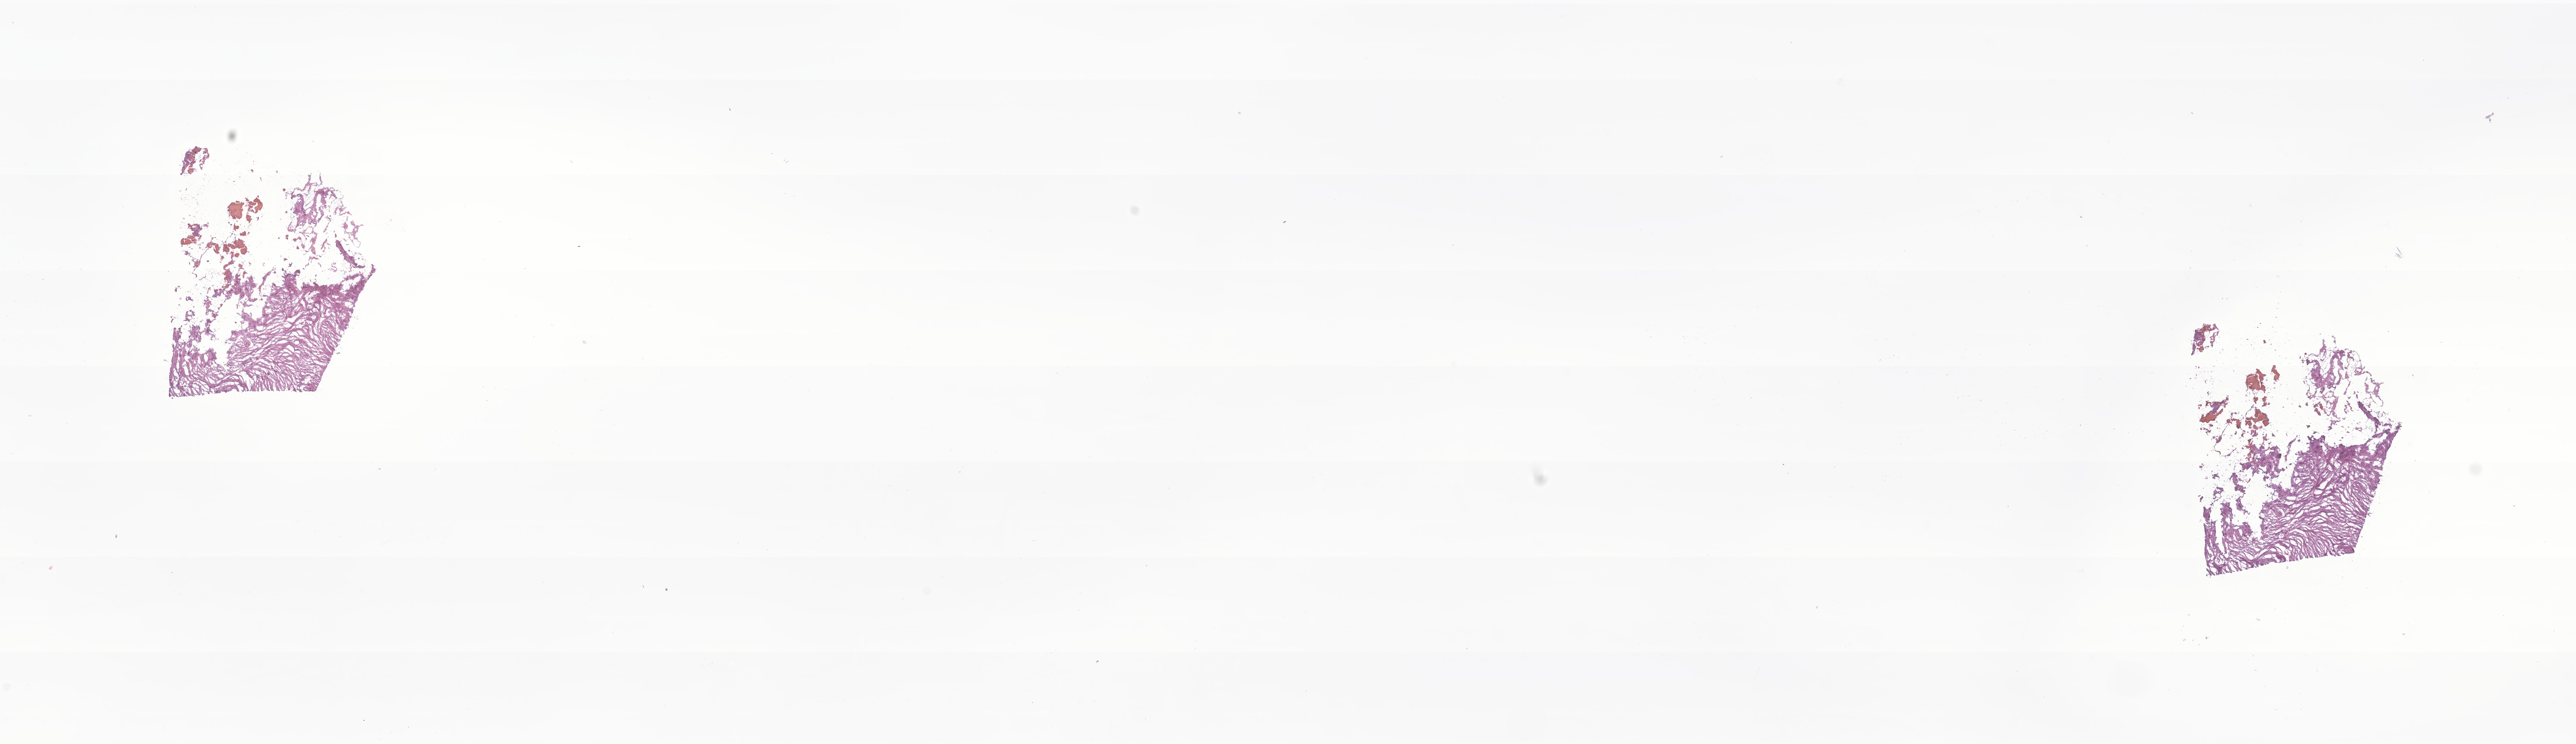
Haematoxylin and eosin whole-slide image of tumor tissue from the brain — shown as a low-resolution overview of the whole scanned area (about 28.8 x 8.3 mm); frozen section. Patient: female, age 206 months.
- recorded diagnosis: Neoplasm, uncertain whether benign or malignant